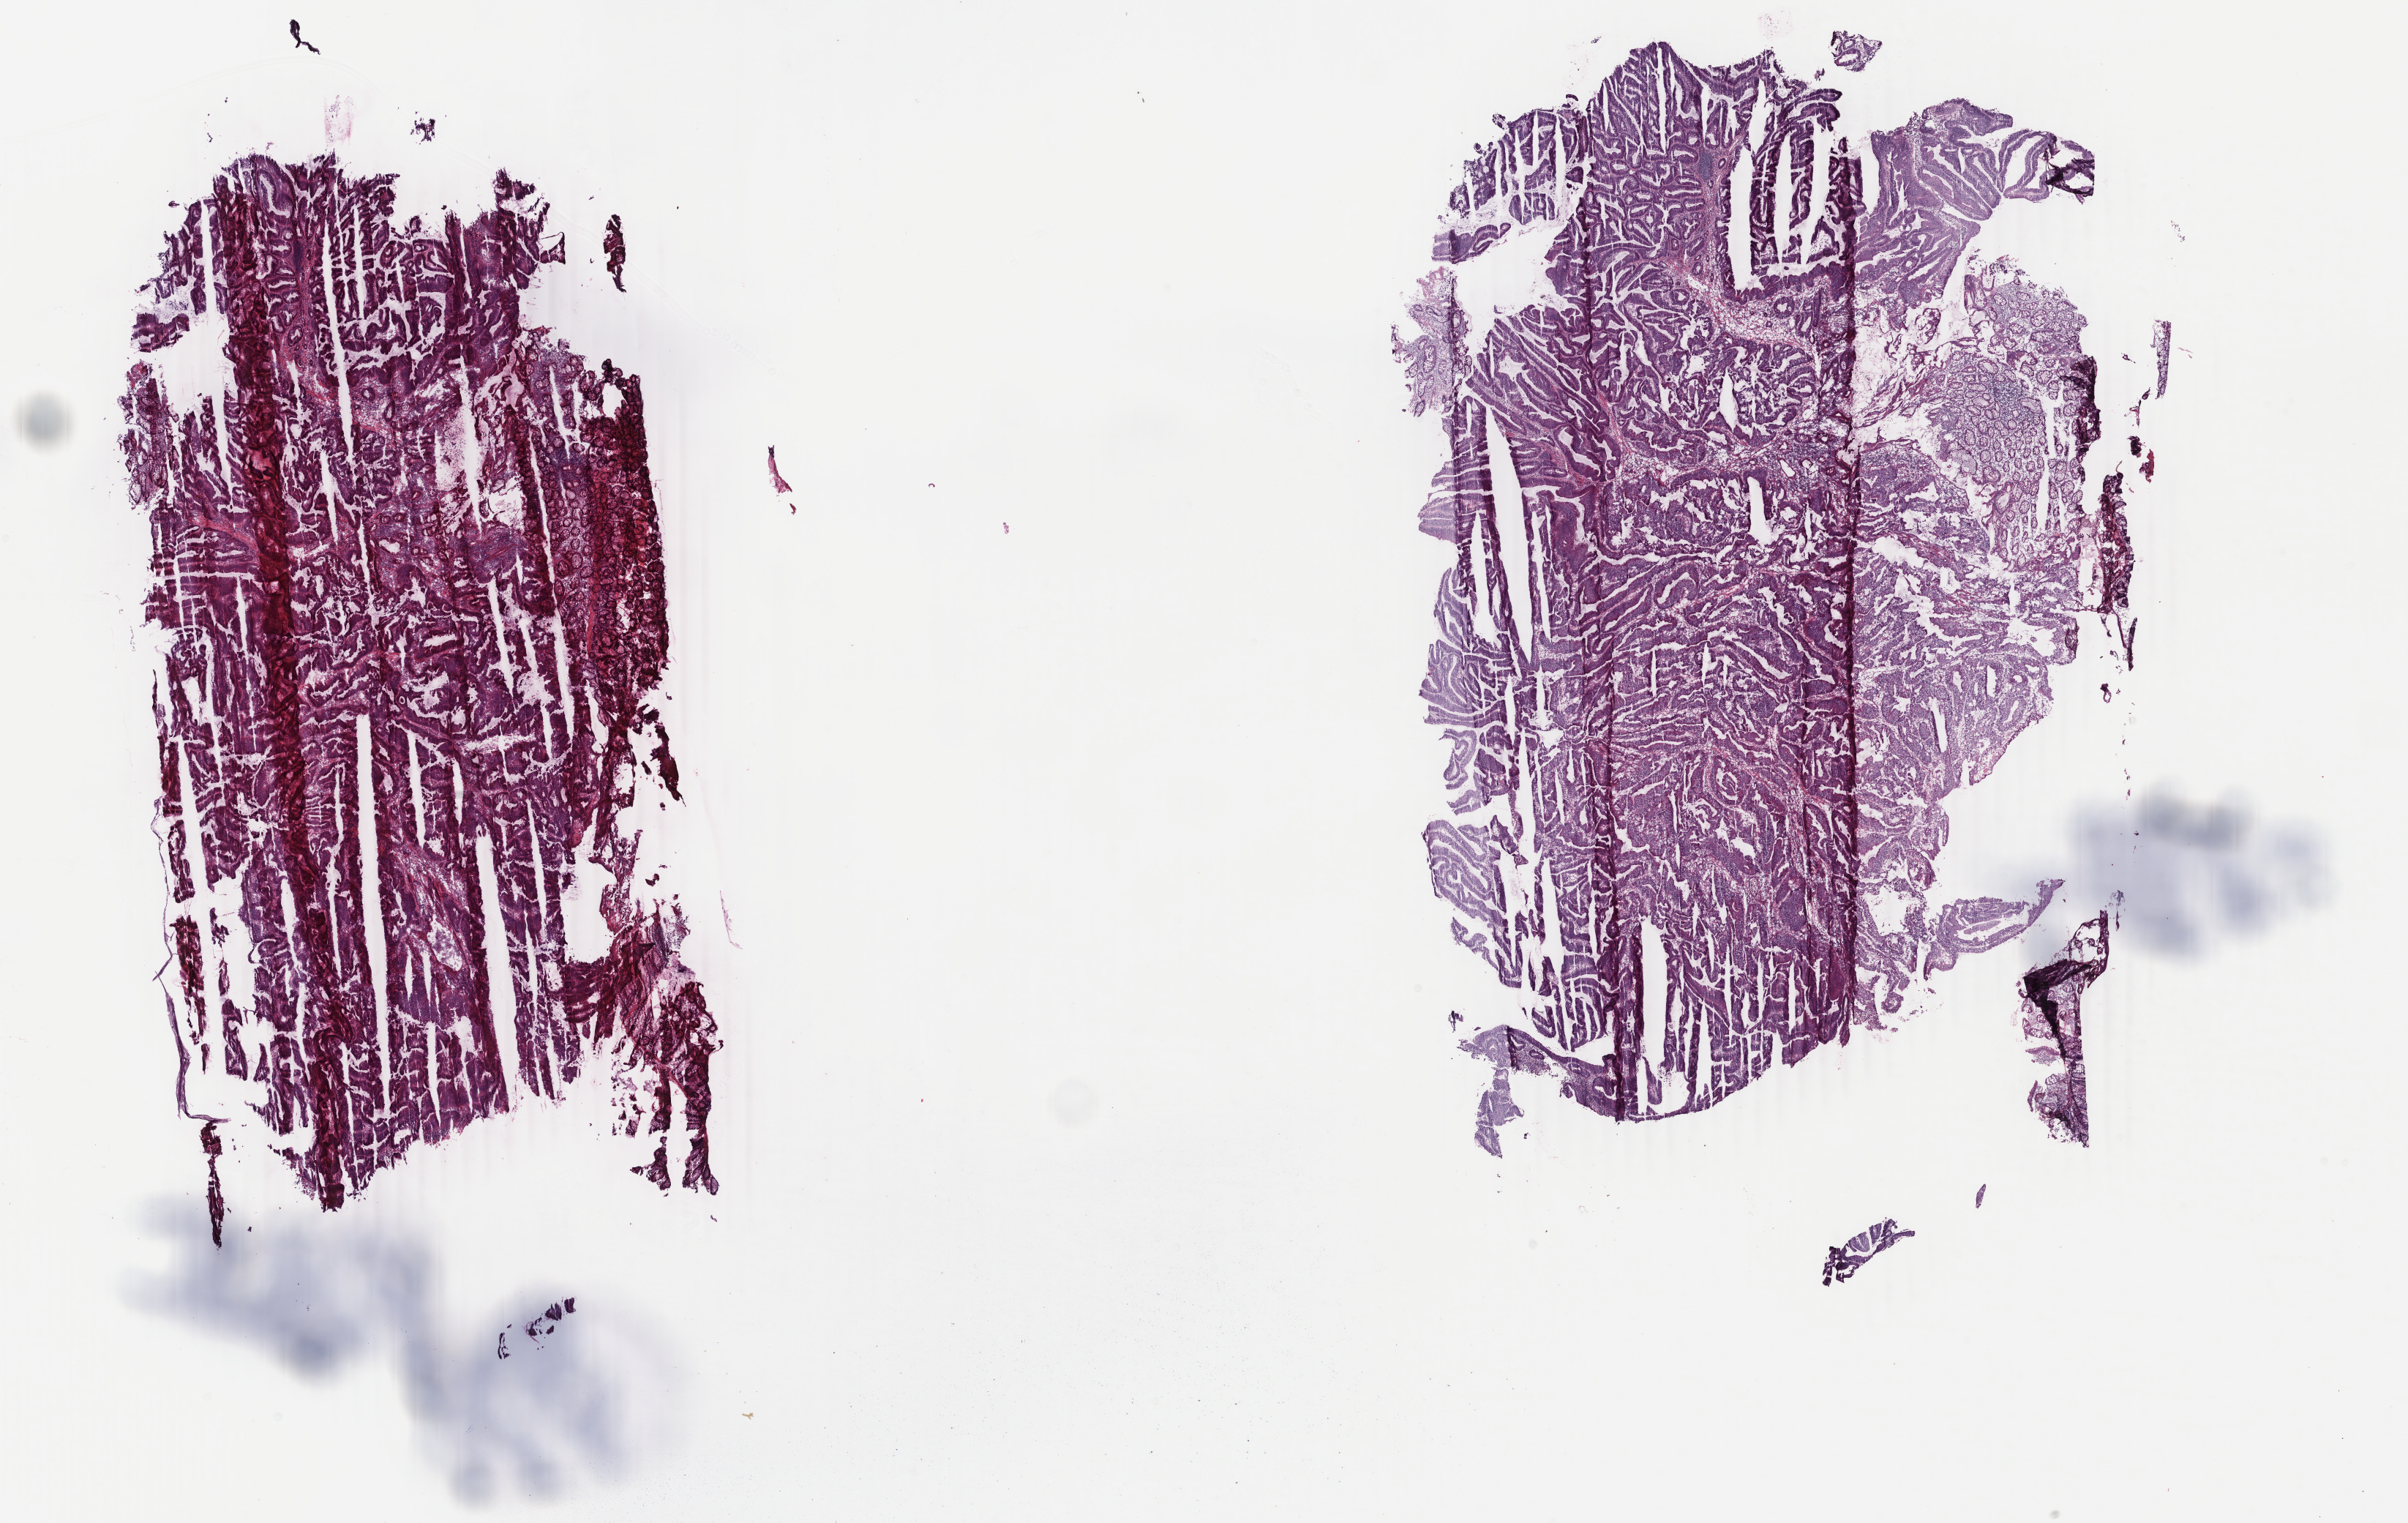
H&E whole-slide image, shown as a low-resolution overview of the whole scanned area (about 26.2 x 16.6 mm). Frozen section from the top of the tissue portion. Sample: primary tumour, colon. Patient: male, age at initial diagnosis 73 years. Slide review estimates, as recorded: tumour cells 79%, tumour nuclei 80%, normal cells 10%, stromal cells 10%, necrosis 1%. Infiltration values recorded for this section: lymphocyte infiltration 8%, monocyte infiltration 0%, neutrophil infiltration 1%.
Lymph nodes positive (case pathology): 0 of 18 examined. Histologic diagnosis: Adenocarcinoma, NOS (cecum). AJCC pathologic stage: I.